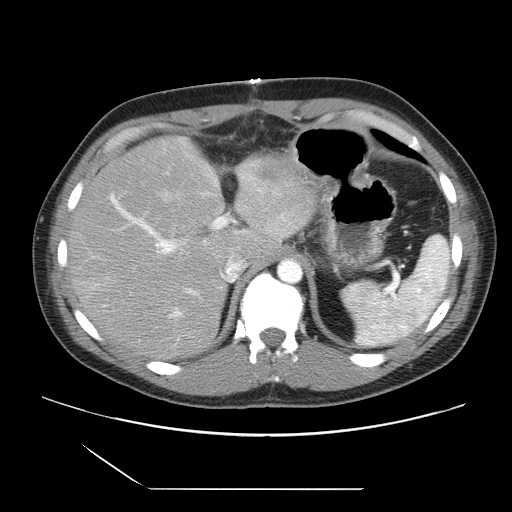
Contrast-enhanced abdominal CT, one axial slice. Slice 20 of 39 in the series (ordered by position). 120 kVp. Intravenous contrast given. Soft-tissue window (W 400 / L 40 HU). 512 × 512 image matrix. Male patient, age 39 years. Case-level facts recorded for this patient, not image findings: diagnosis: colorectal cancer liver metastases, imaged before liver resection; multiple liver metastases: yes; largest metastasis: 1.3 cm.
Annotated regions visible in this slice (expert manual segmentation):
- hepatic veins: box from (x=167, y=255) to (x=245, y=308) px
- liver: (x=67, y=138)–(x=316, y=360)
- planned liver remnant (the part of the liver to remain after resection): (x=116, y=138)–(x=316, y=262)
- portal vein (with intrahepatic branches): (x=102, y=174)–(x=263, y=320)